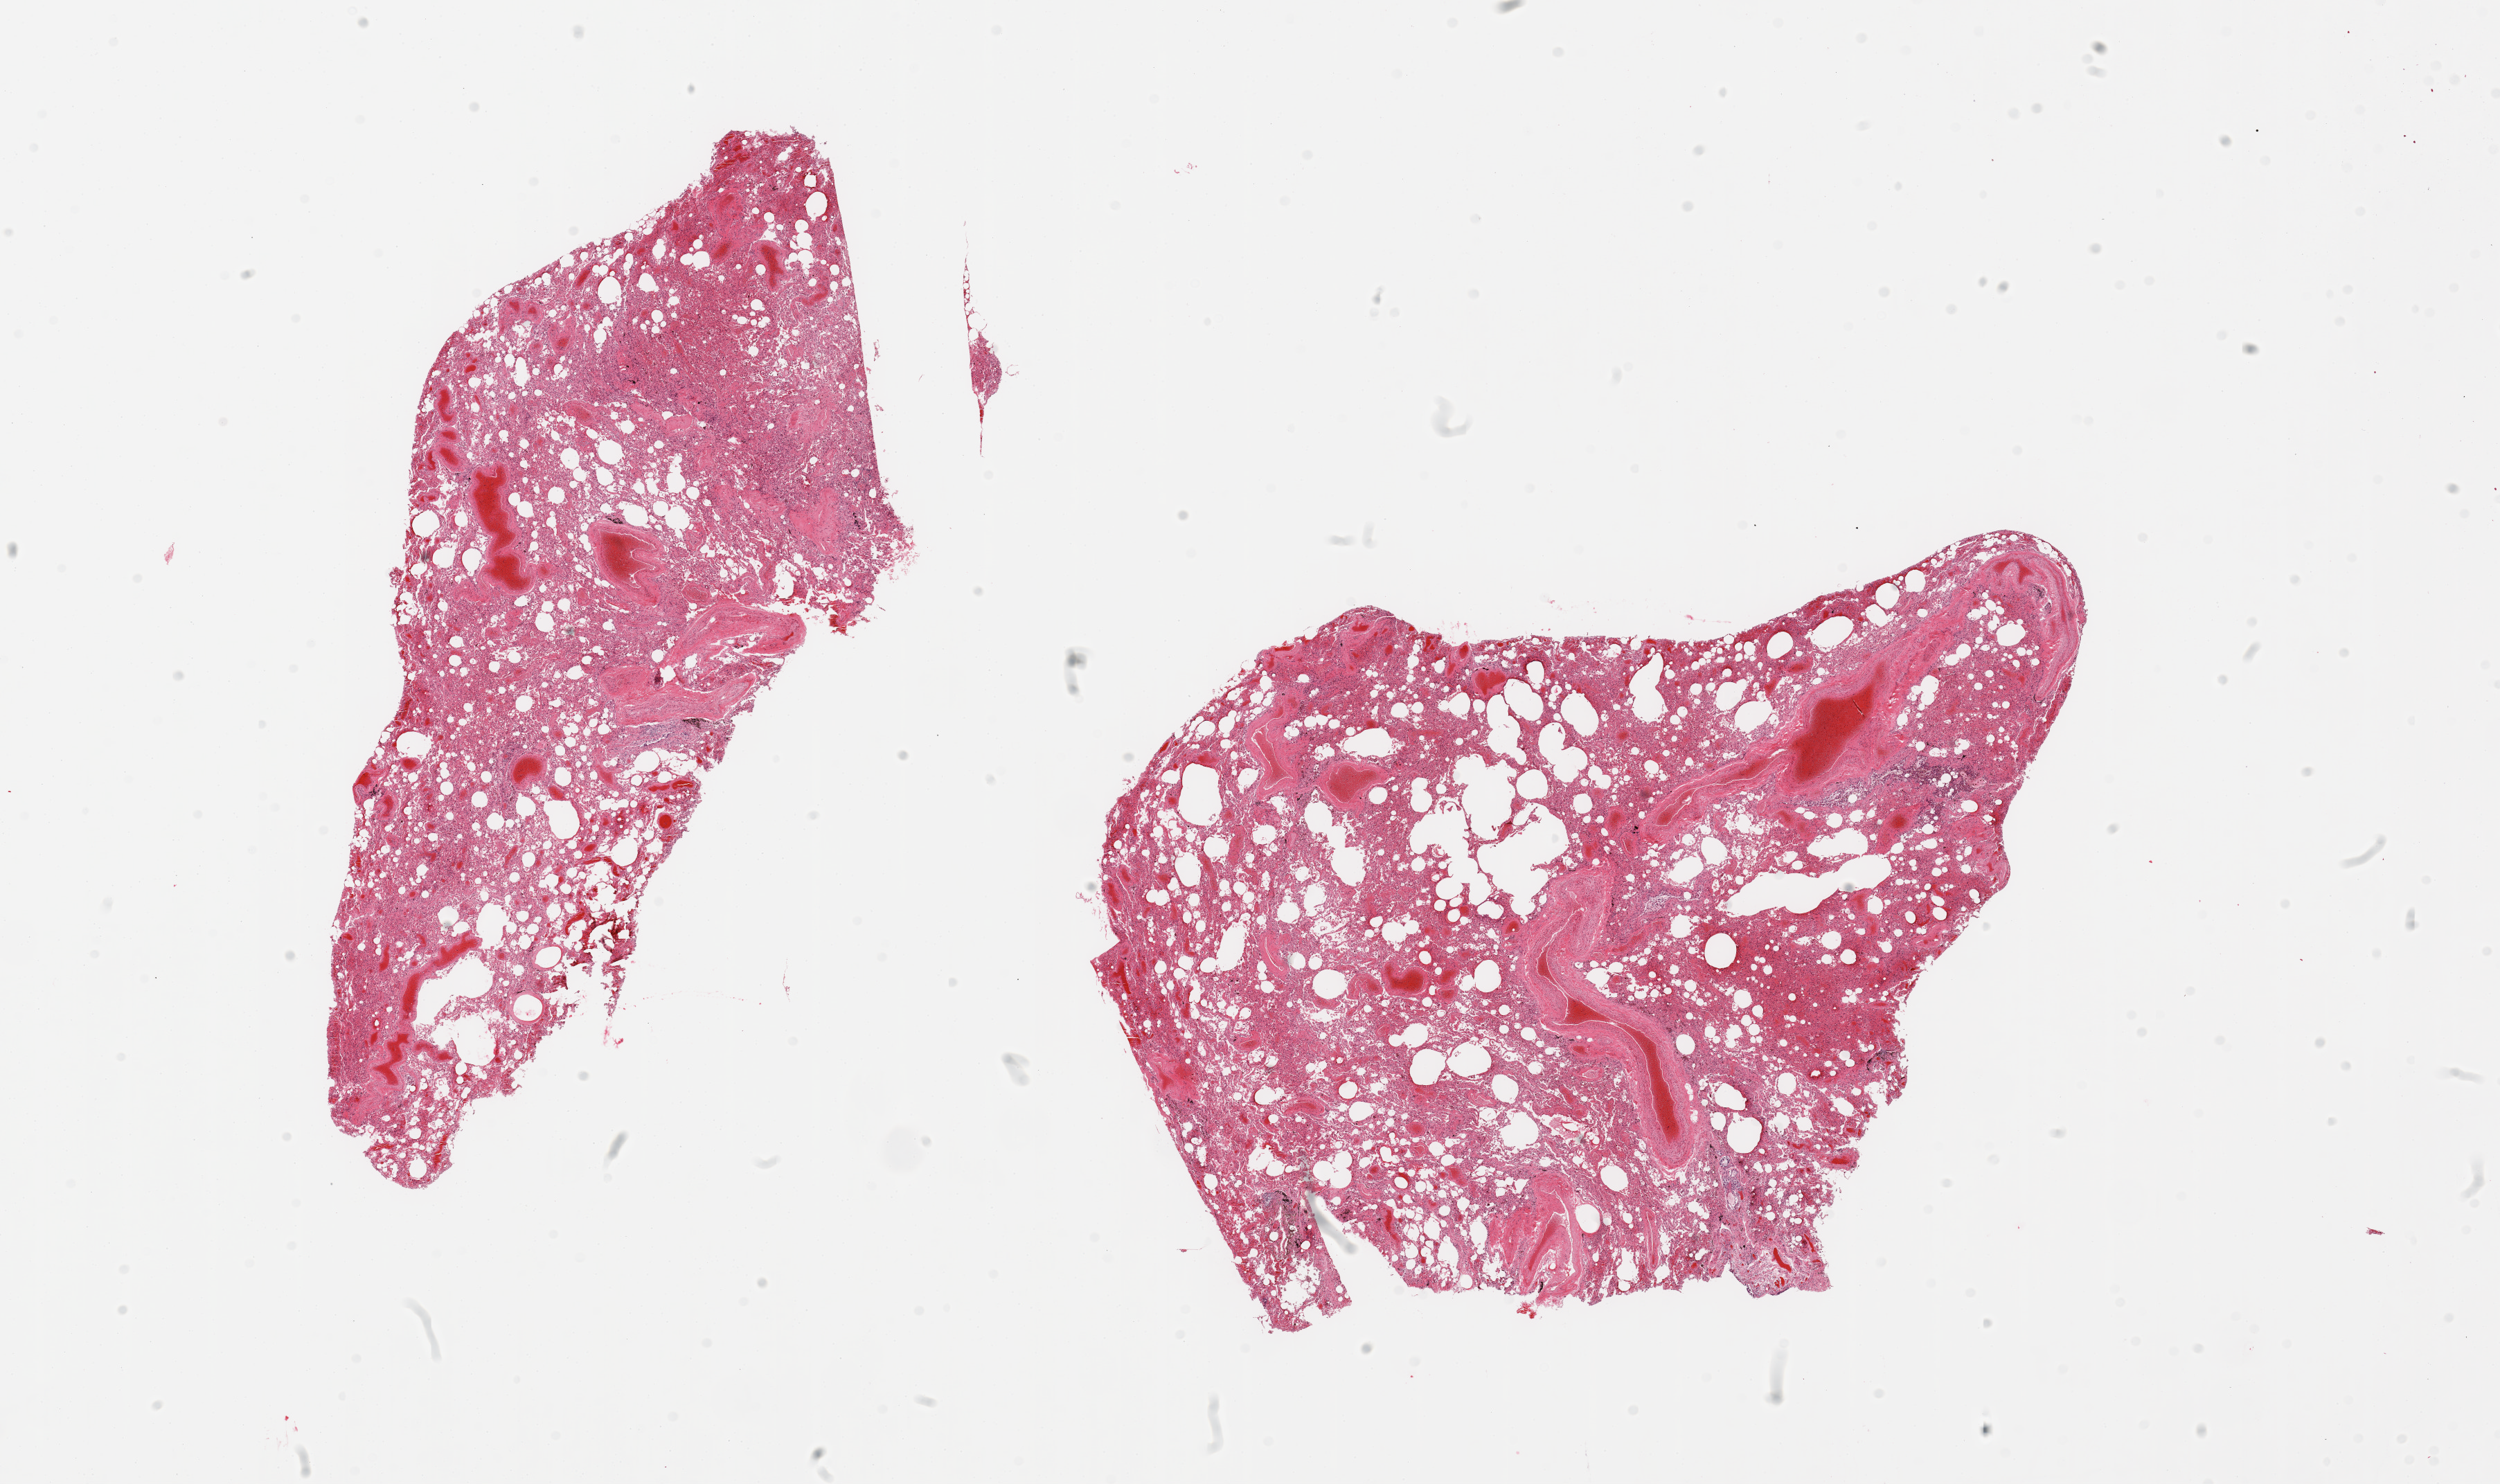
Whole-slide image, hematoxylin and eosin (H&E) stain, shown as a low-resolution overview of the whole scanned area (about 28.5 x 16.9 mm, acquisition: 20x scan), PAXgene-fixed paraffin-embedded (PFPE) section, section of lung (target tissue), donor tissue sample. Donor sex: male.
Review note (as recorded): 2 pieces; congested, scattered emphysema.